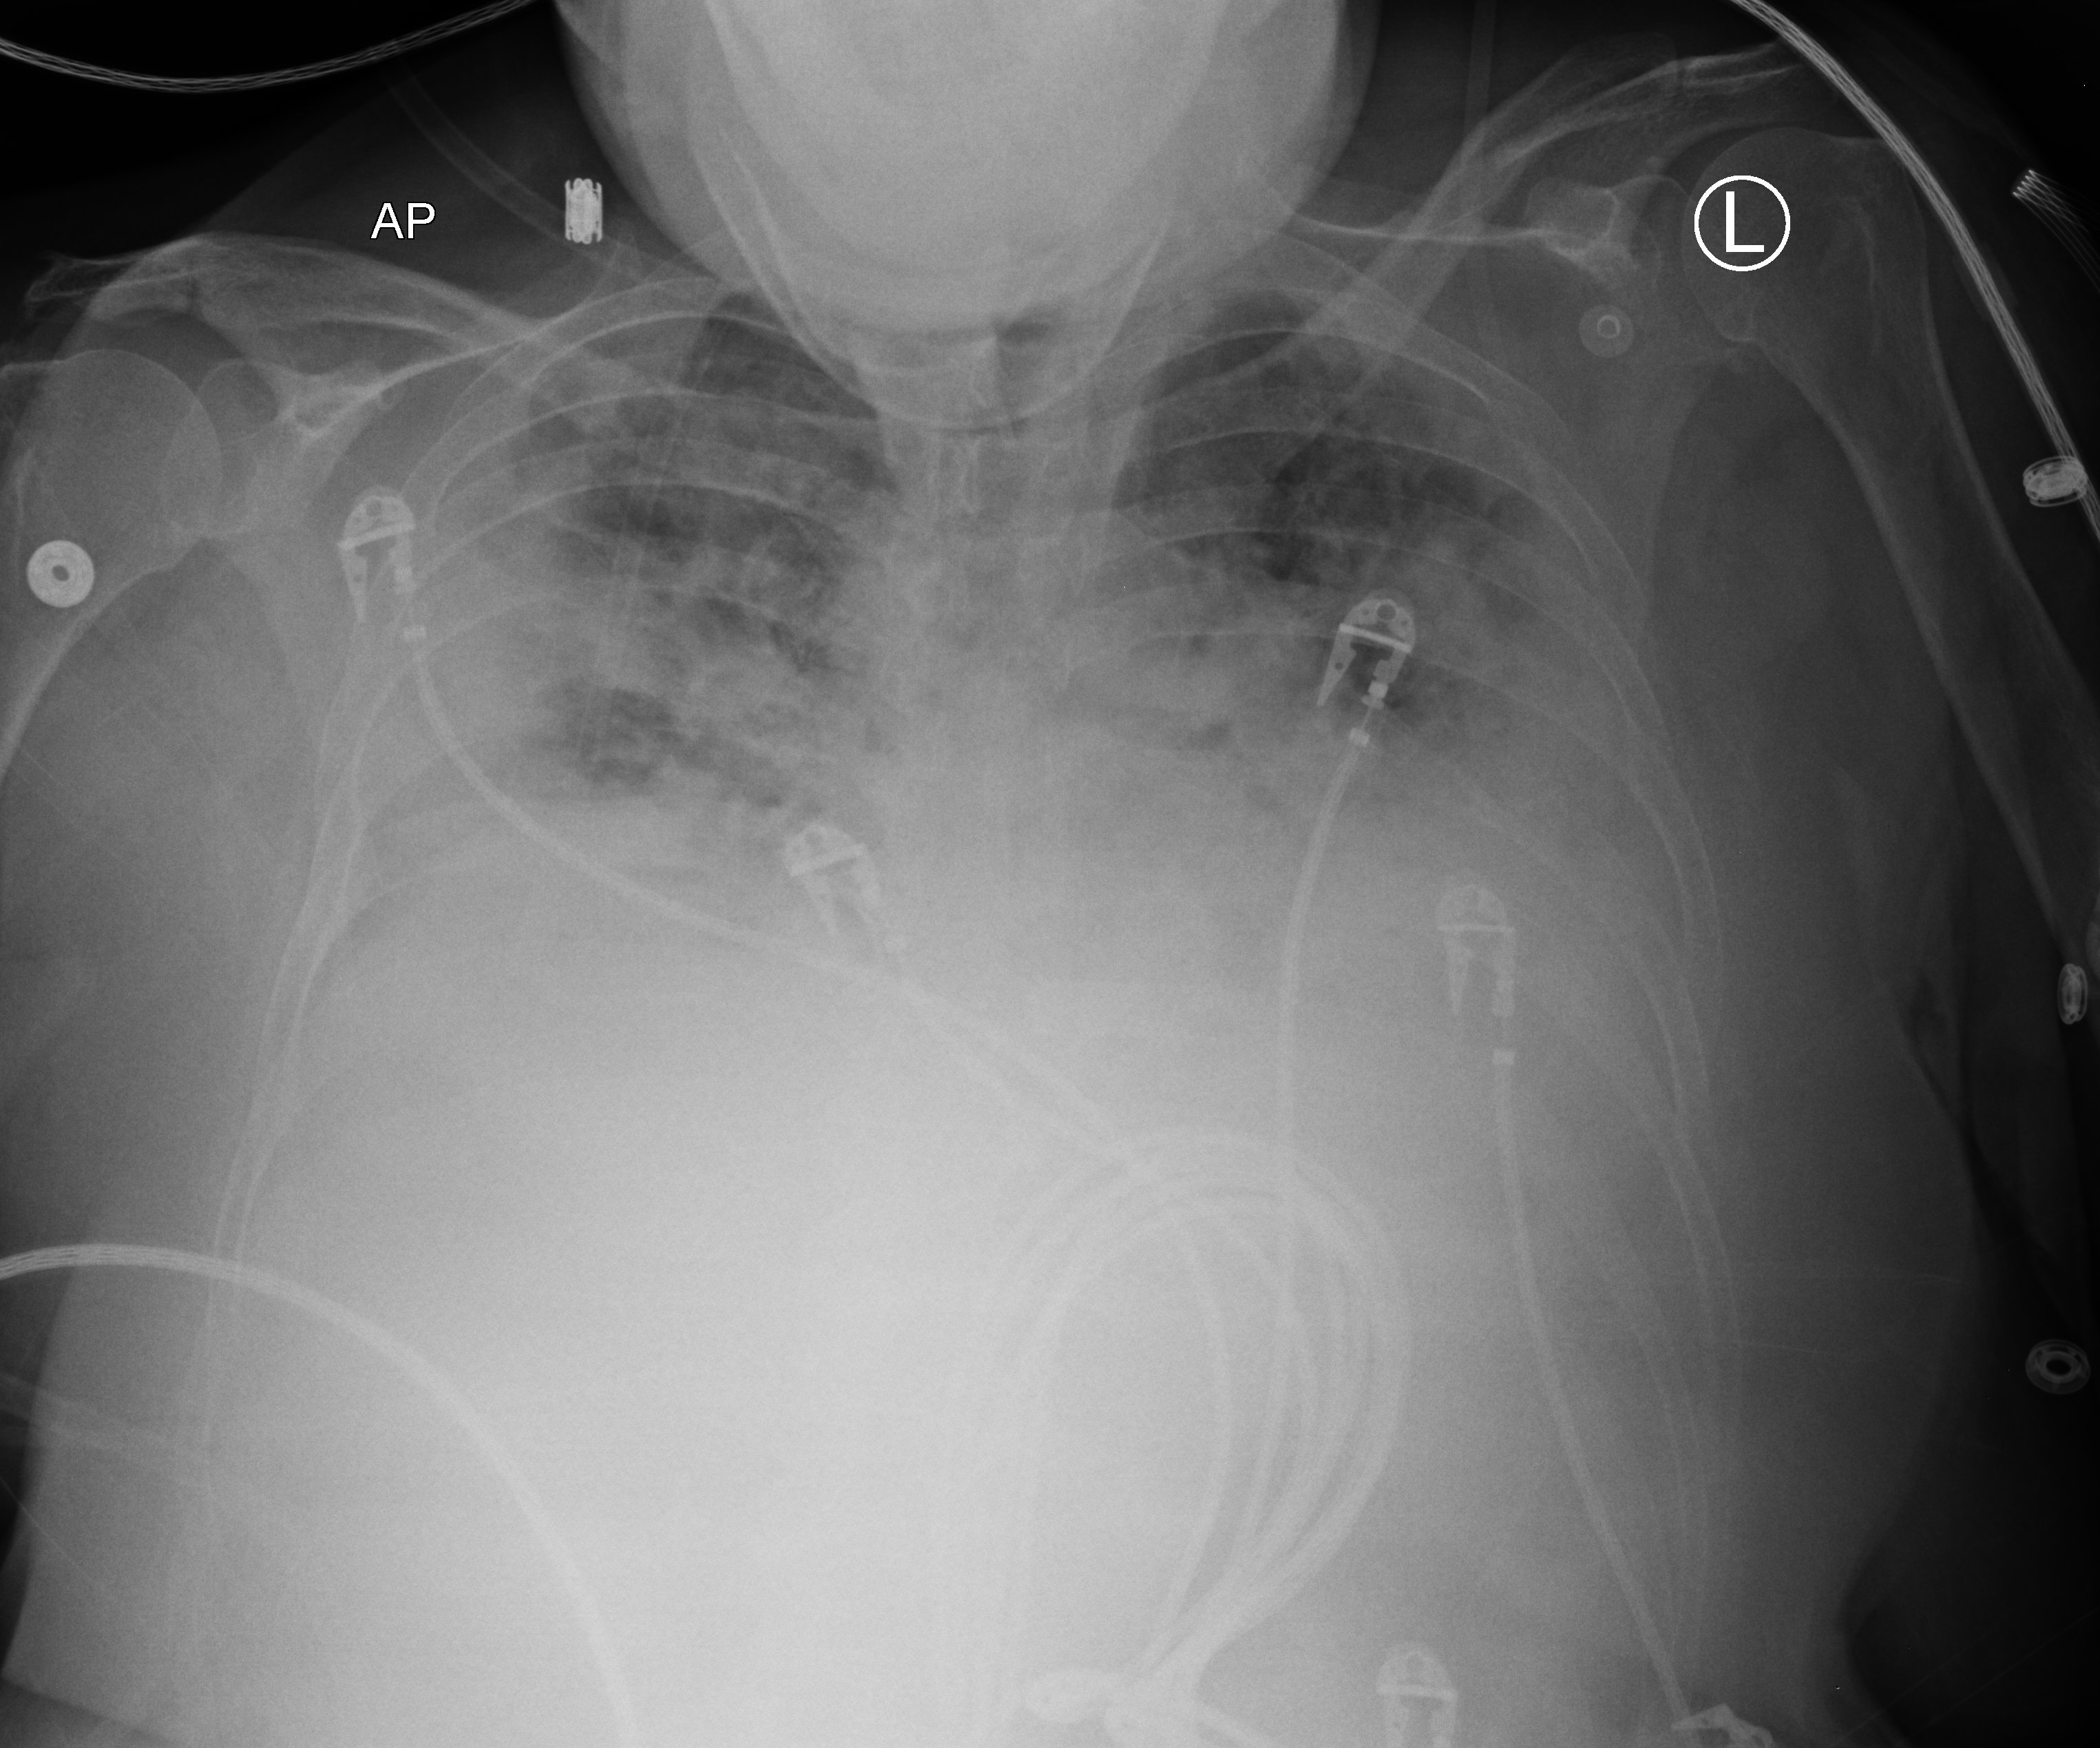
Chest X-ray (portable); anteroposterior (AP) projection. Female patient hospitalised with COVID-19, age 18–59 years.
Admission-level facts for this patient (not findings on this image; timing relative to this image not recorded):
- admitted to intensive care during this hospital stay: yes